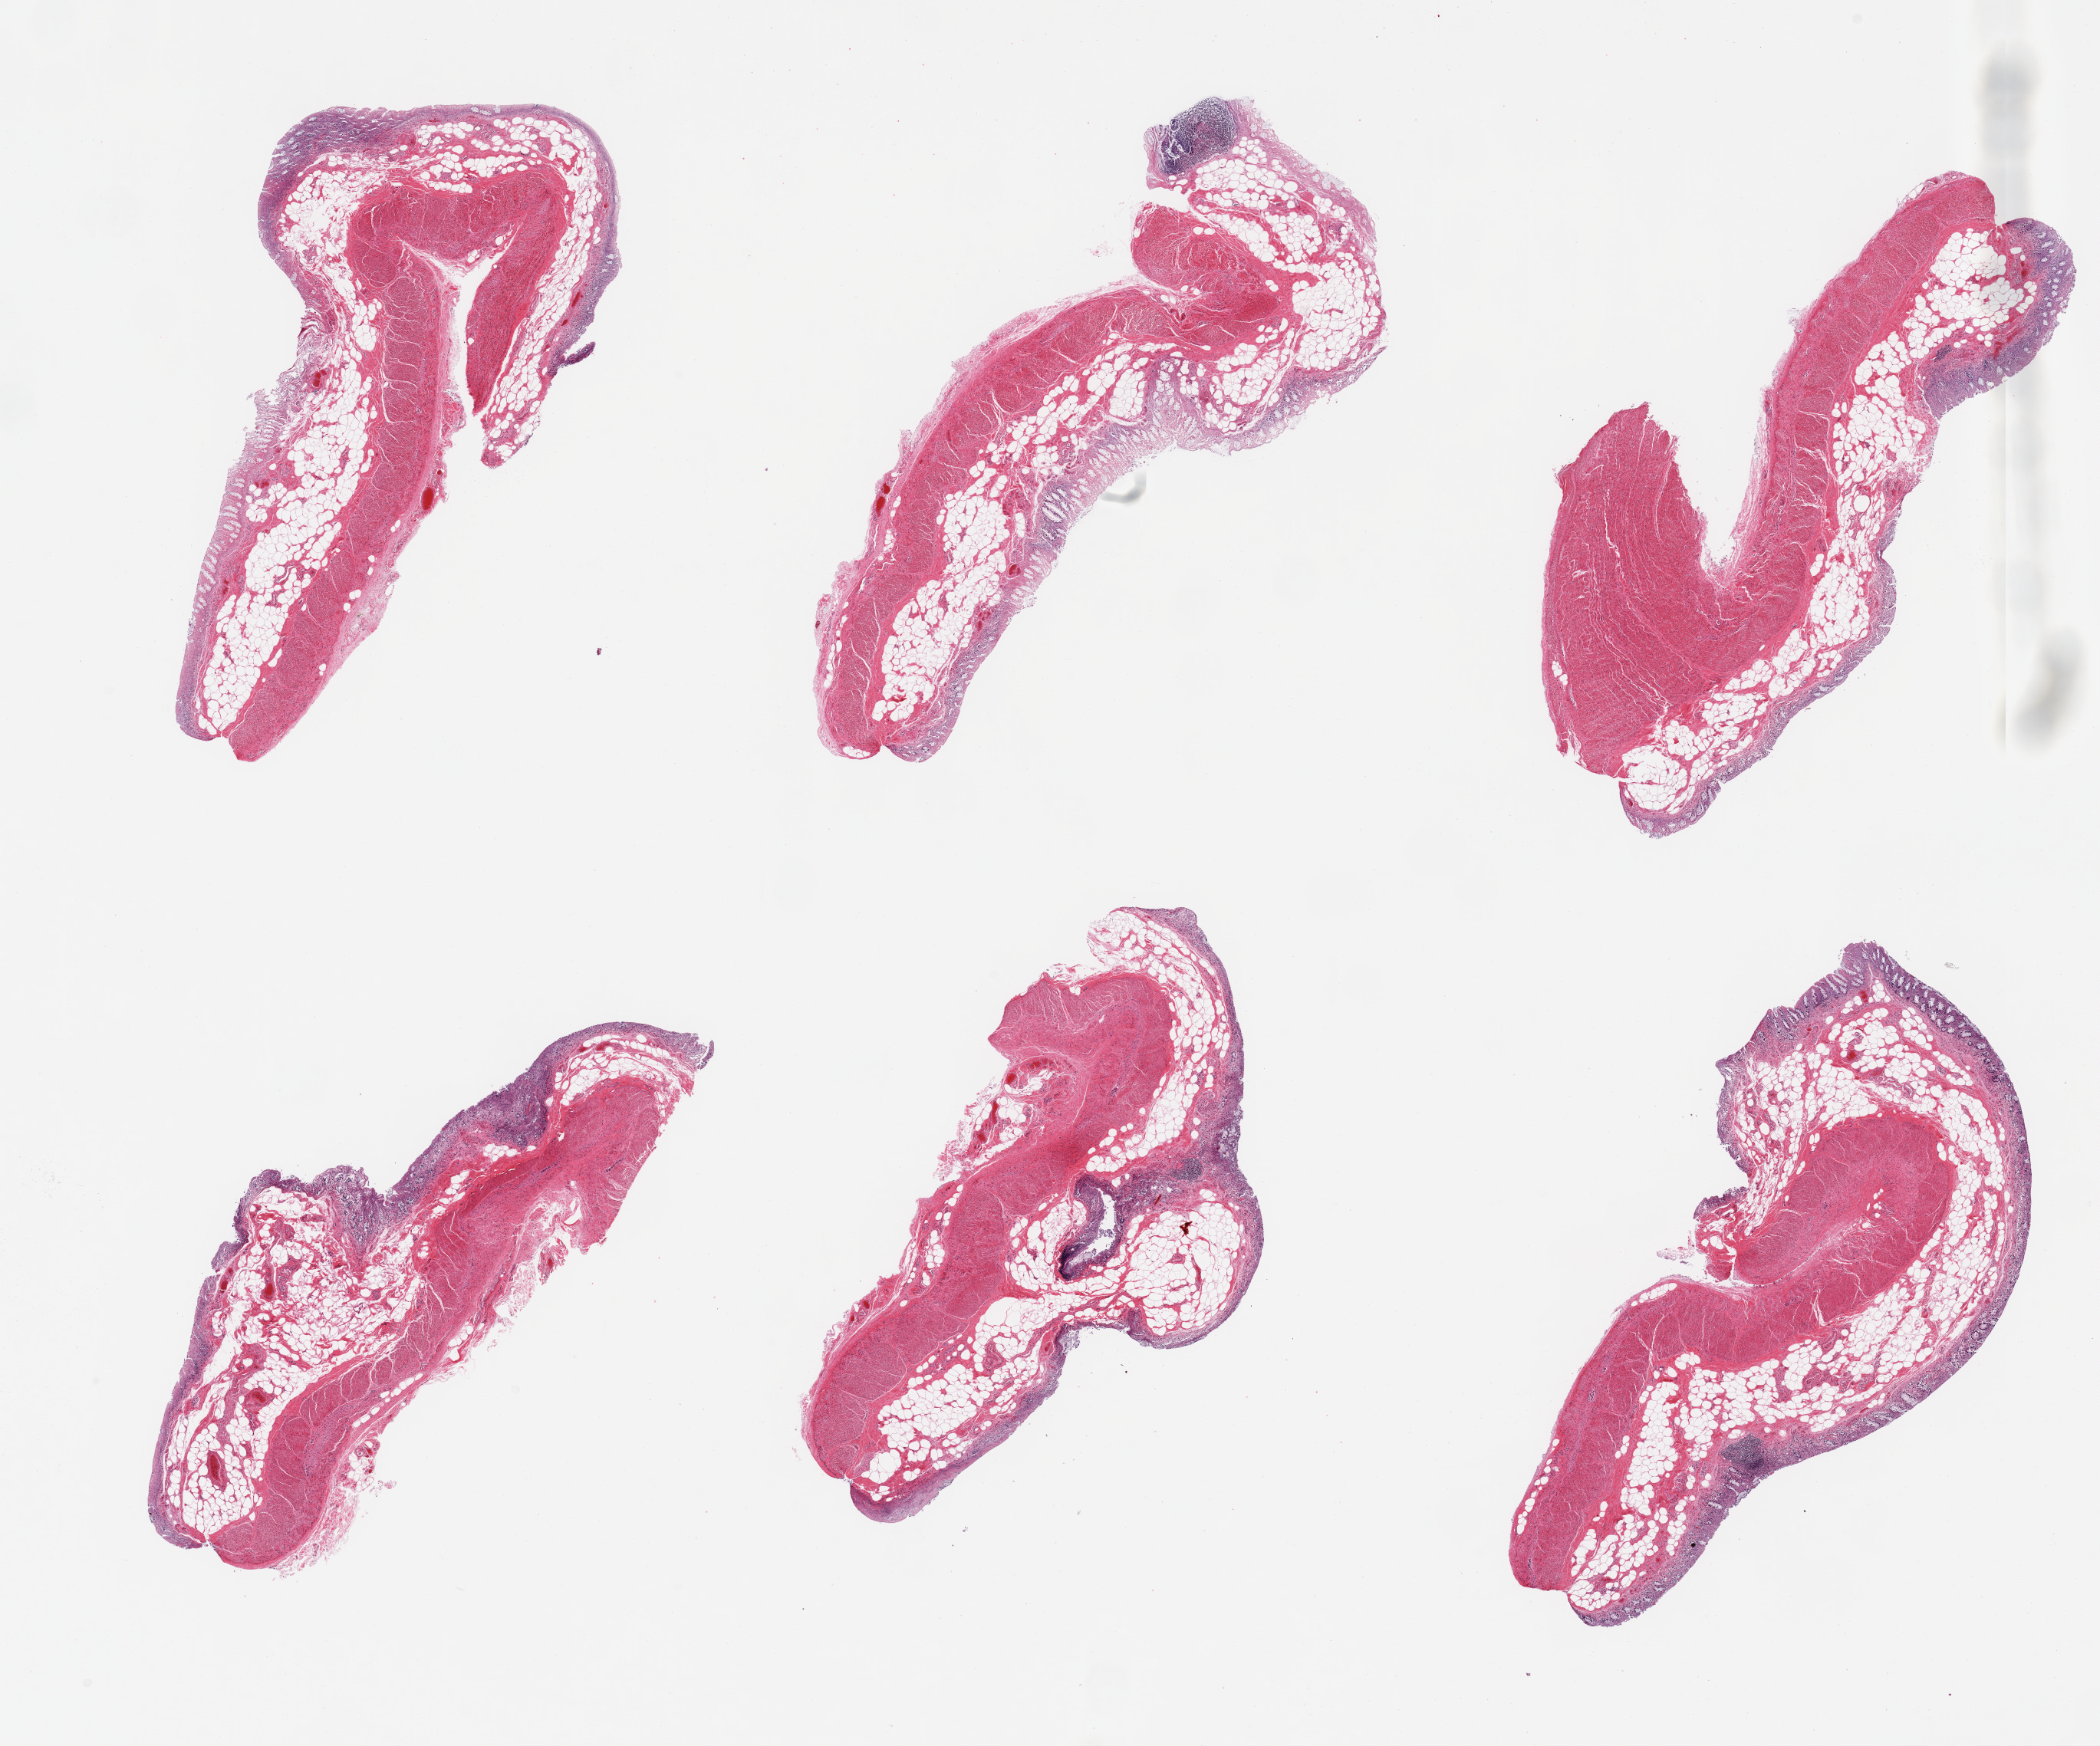
Haematoxylin and eosin whole-slide image, brightfield, shown as a low-resolution overview of the whole scanned area (about 21.7 x 18.0 mm, slide scanned at 20x), PAXgene-fixed, paraffin-embedded tissue, section of transverse colon (target tissue), tissue donor sample.
Pathologist's review note for this sample: 6 pieces, mucosa with advance autolysis, partially sloughed.